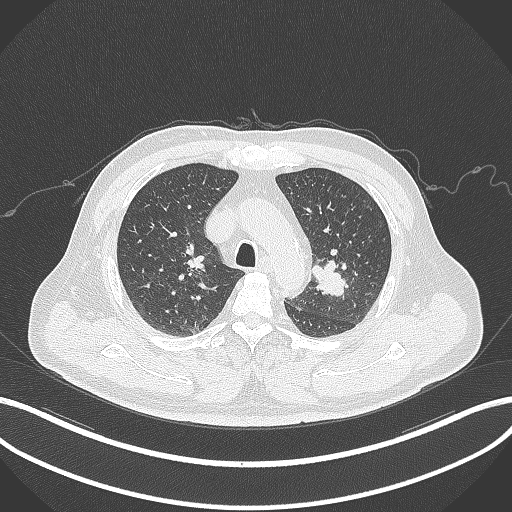
Chest CT, one axial slice; position 224 of 286 along the scan axis; 120 kVp; lung window (W 1500 / L -600 HU); 512 × 512 image matrix, field of view 400 × 400 mm. Patient: male, 67 years. Case-level facts recorded for this patient, not image findings: clinical TNM (as recorded): T2a N1 M0; histopathological grade: G3.
Structures marked on this image (rectangle marked by the reading radiologist):
- lung tumour (recorded histology: adenocarcinoma): box from (x=309, y=258) to (x=349, y=298) px